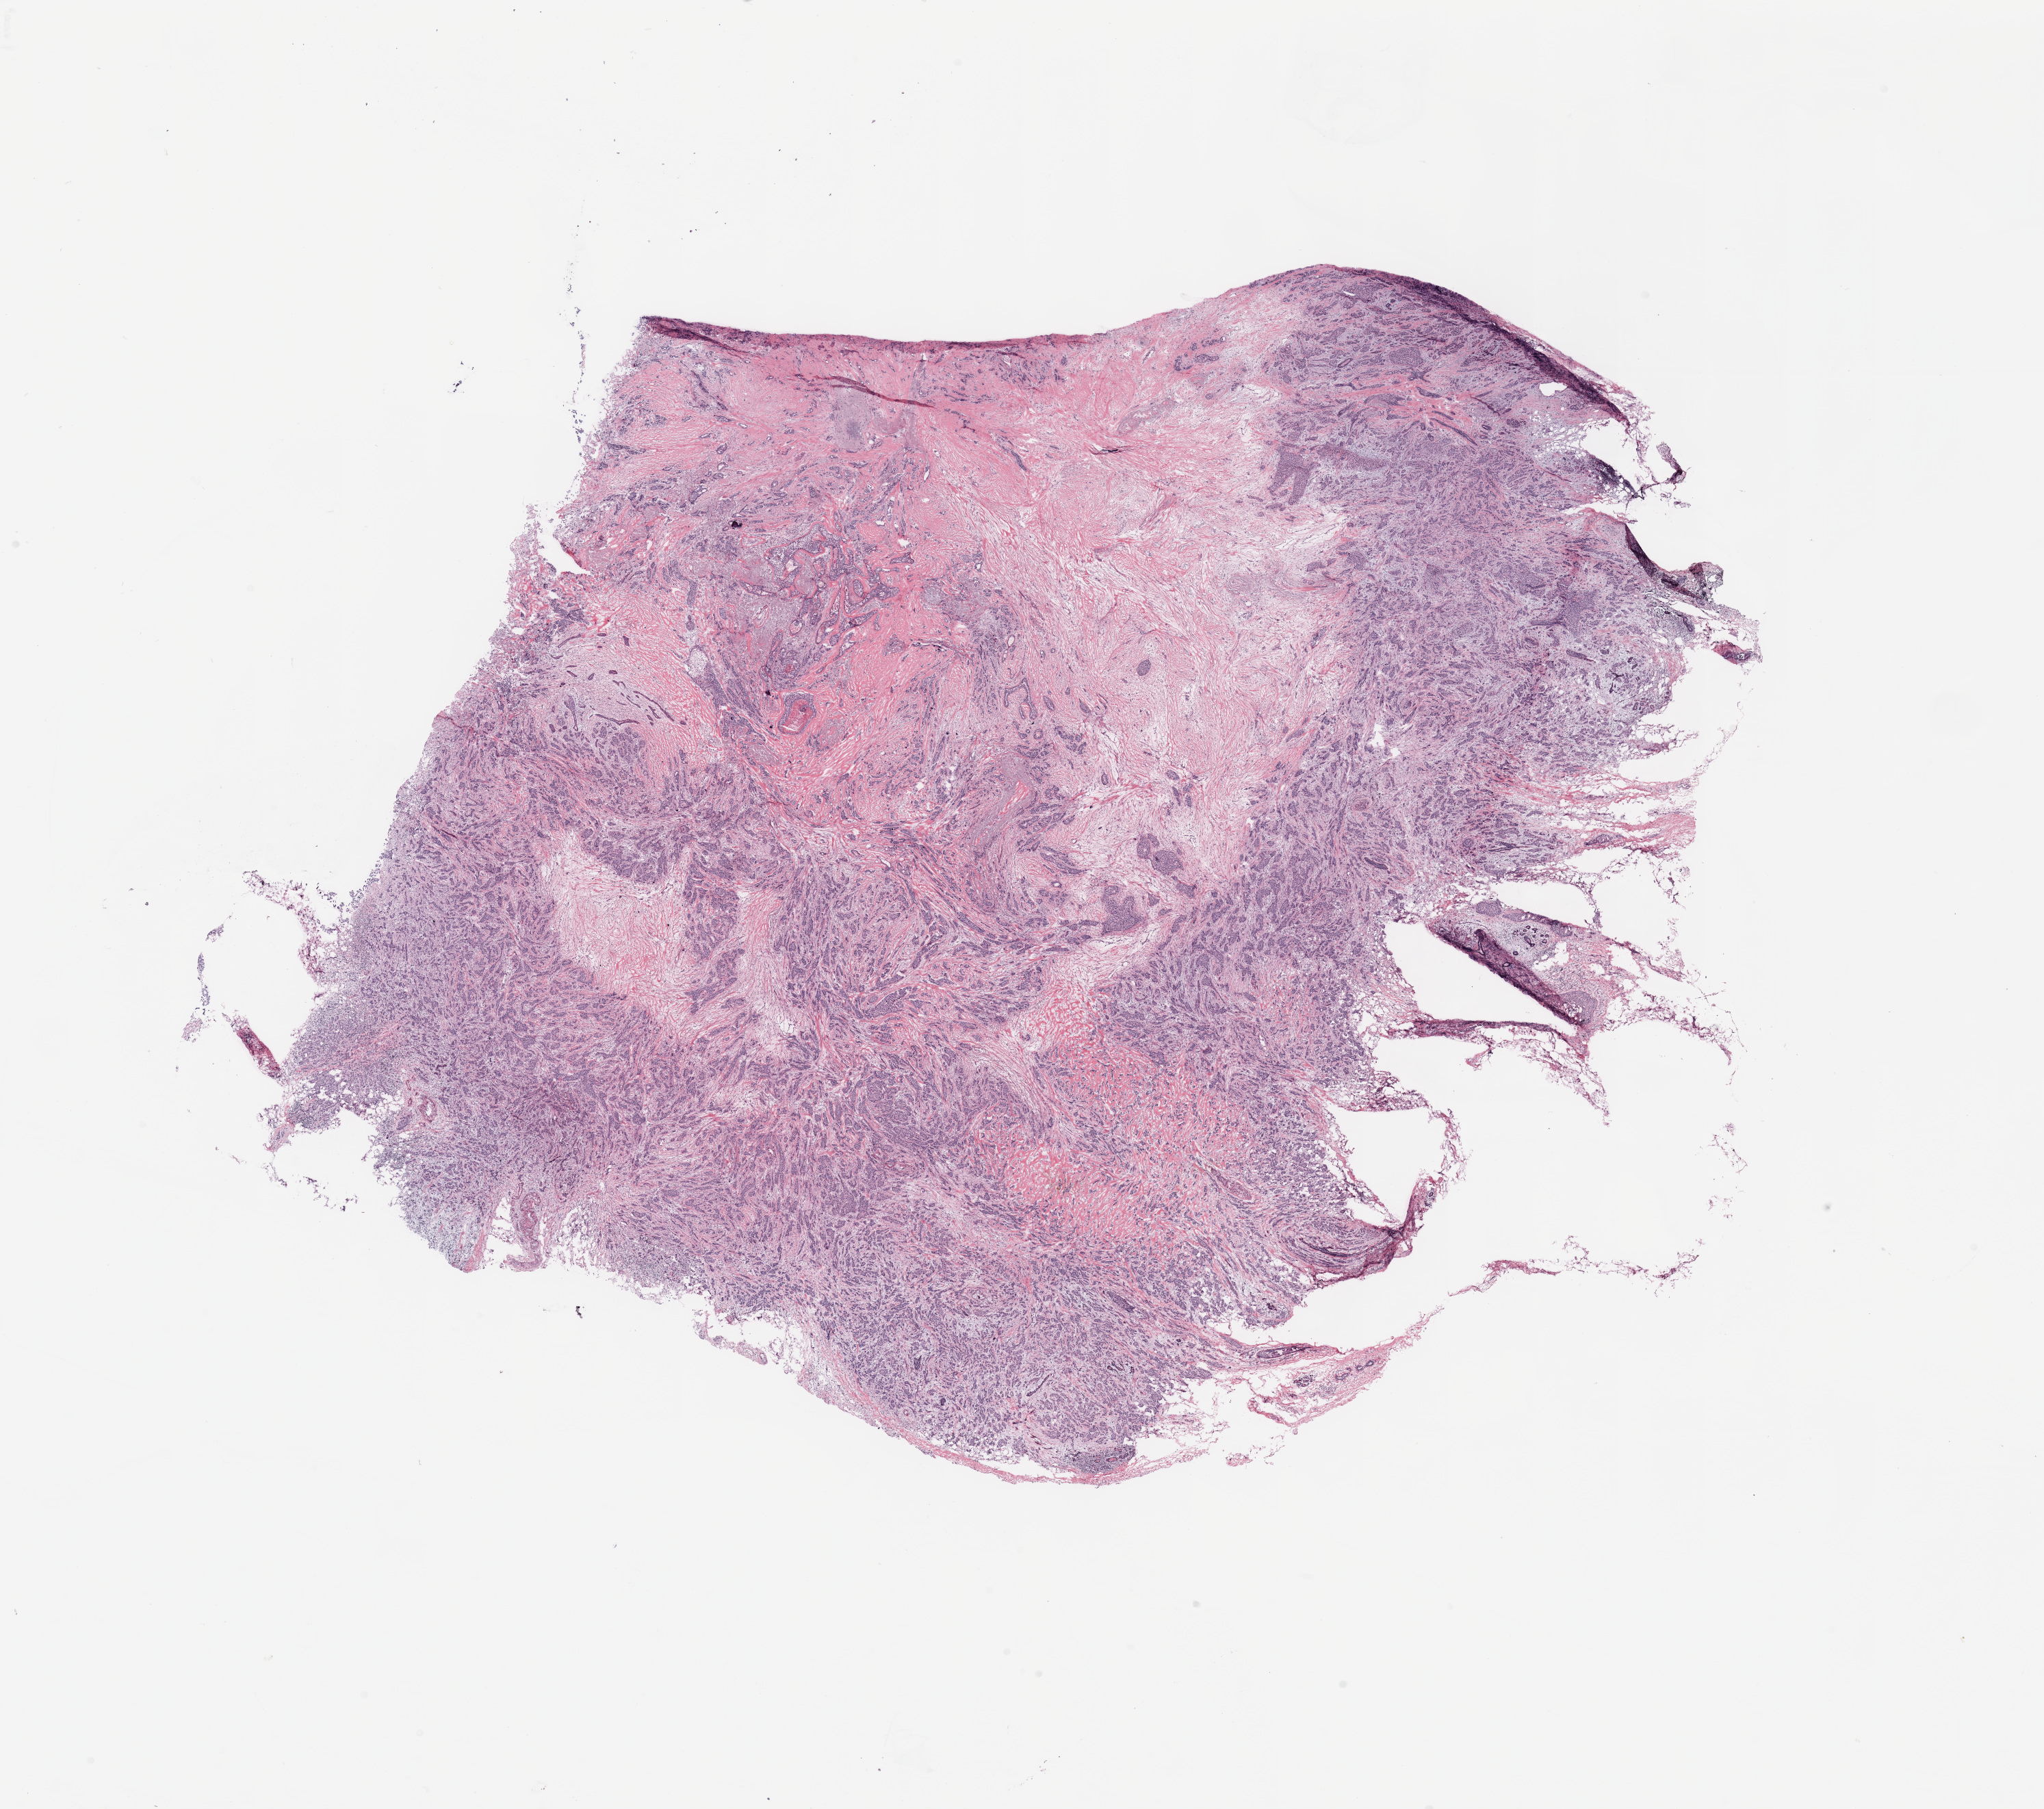
Hematoxylin and eosin (H&E) stained whole-slide image — whole scanned area (about 23.6 x 20.9 mm, acquisition: 20x scan) shown as a low-resolution overview. Breast, tissue type not recorded.
* patient diagnosis (cohort enrolment): breast cancer (breast)